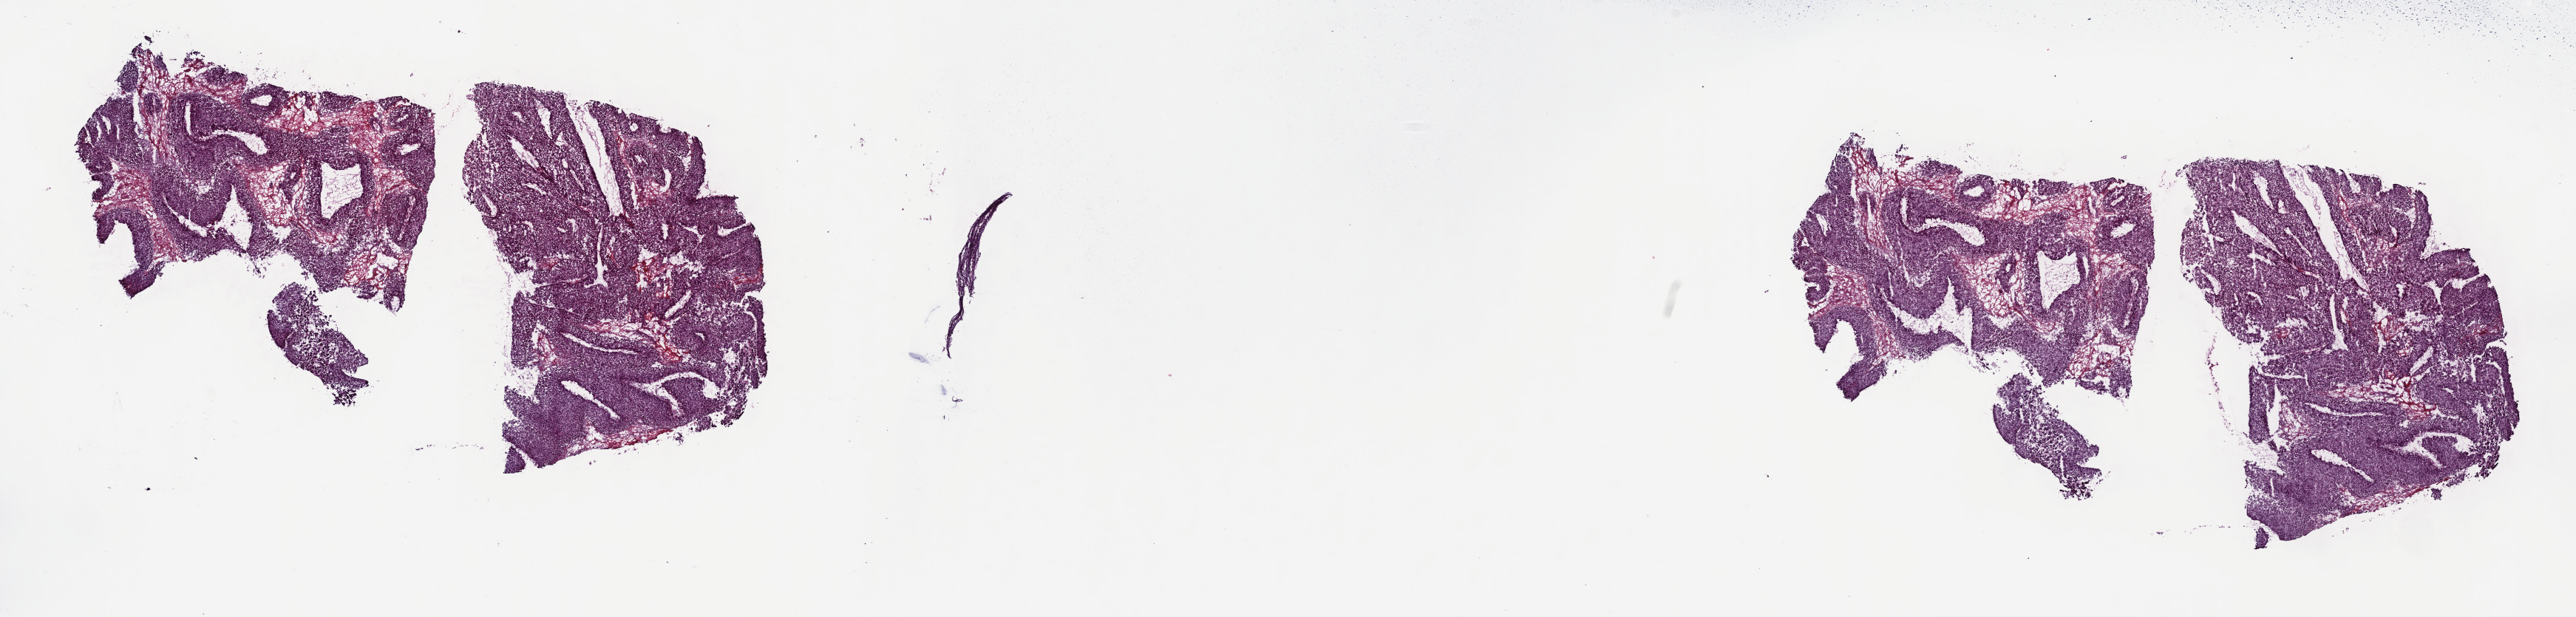
Whole-slide histology image, H&E, shown as a low-resolution overview of the whole scanned area (about 28.2 x 6.8 mm, slide scanned at 40x); frozen section; sample: primary tumour, liver. Patient: female, age at initial diagnosis 73 years. Histologic grade: G2 (moderately differentiated). Composition of this section per pathologist review: tumour cells 75%, tumour nuclei 95%, normal cells 0%, stromal cells 5%, necrosis 20%. Inflammatory infiltration, as recorded: lymphocyte infiltration 3%, monocyte infiltration 1%, neutrophil infiltration 0%.
• diagnosis: Hepatocellular carcinoma, NOS
• TNM: T1 N0 M0
• AJCC pathologic stage: I